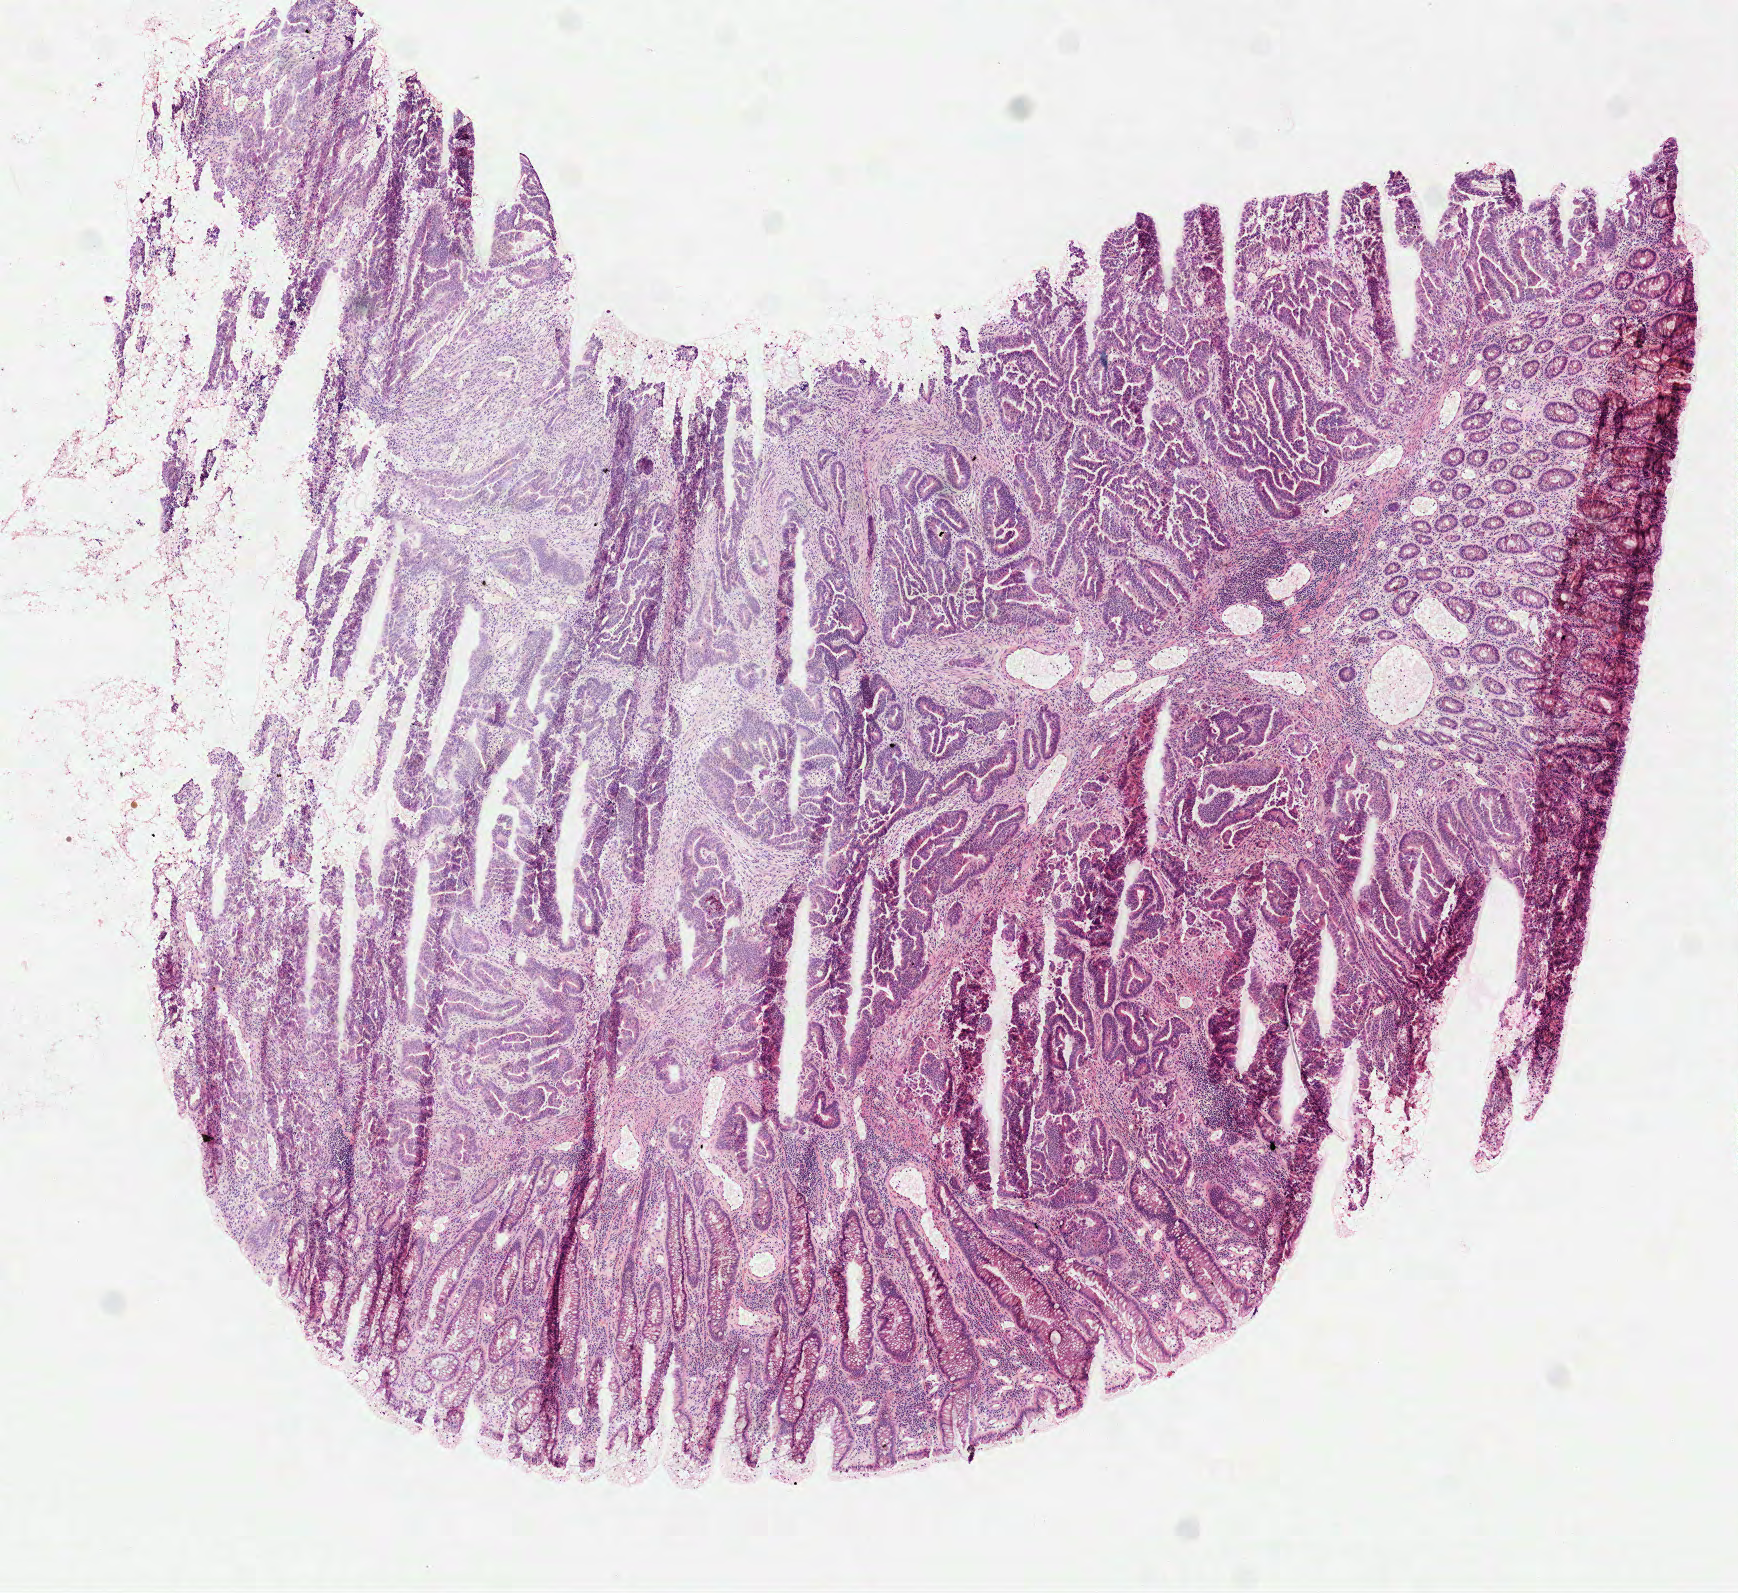
Digitized Hematoxylin and eosin (H&E) stained tissue section (whole slide), a low-resolution overview of the entire scanned area, about 7.0 x 6.4 mm (acquisition: 40x scan). Frozen section from the top of the tissue portion. Rectum, primary tumour sample. Male patient; age at initial diagnosis 71 years. Composition of this section per pathologist review: tumour cells 70%, tumour nuclei 70%, normal cells 15%, stromal cells 15%, necrosis 0%.
- histologic diagnosis: Tubular adenocarcinoma
- AJCC pathologic stage: IIIA
- lymph nodes positive (case pathology): 3 of 8 examined